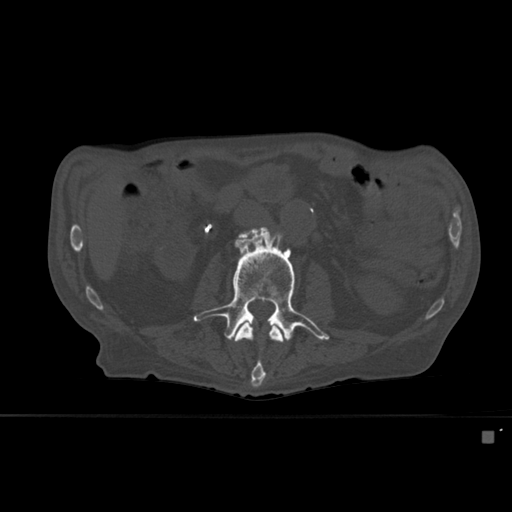
CT including the spine, one axial slice; slice 218 of 527 in the series (ordered by position); bone window (W 1800 / L 400 HU); 512 × 512 image matrix. Male patient, age 78 years. From the clinical record (not read from this slice): primary cancer: prostate.
Outlined on this slice (semi-automatically segmented with operator editing):
- L2 vertebra: bounding box (x1, y1, x2, y2) in pixels: (232, 322, 283, 388)
- L3 vertebra: (193, 227, 330, 341)
- L4 vertebra: (239, 227, 264, 238)